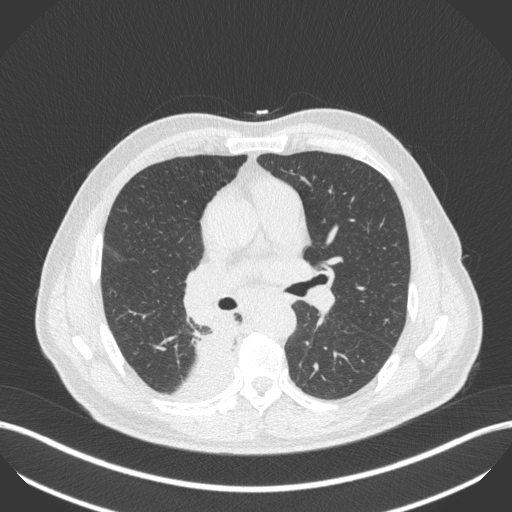
Chest CT, one axial slice; position 266 of 451 along the scan axis; lung window (W 1500 / L -600 HU); 1 mm slice thickness; 512 × 512 image matrix. Patient: male, 61 years. Case-level facts recorded for this patient, not image findings: clinical TNM (as recorded): T1 N0 M0; histopathological grade: G3.
Outlined on this slice (rectangle marked by the reading radiologist):
- lung tumour (recorded histology: small cell carcinoma): bounding box [x1, y1, x2, y2] px = [192, 318, 236, 364]